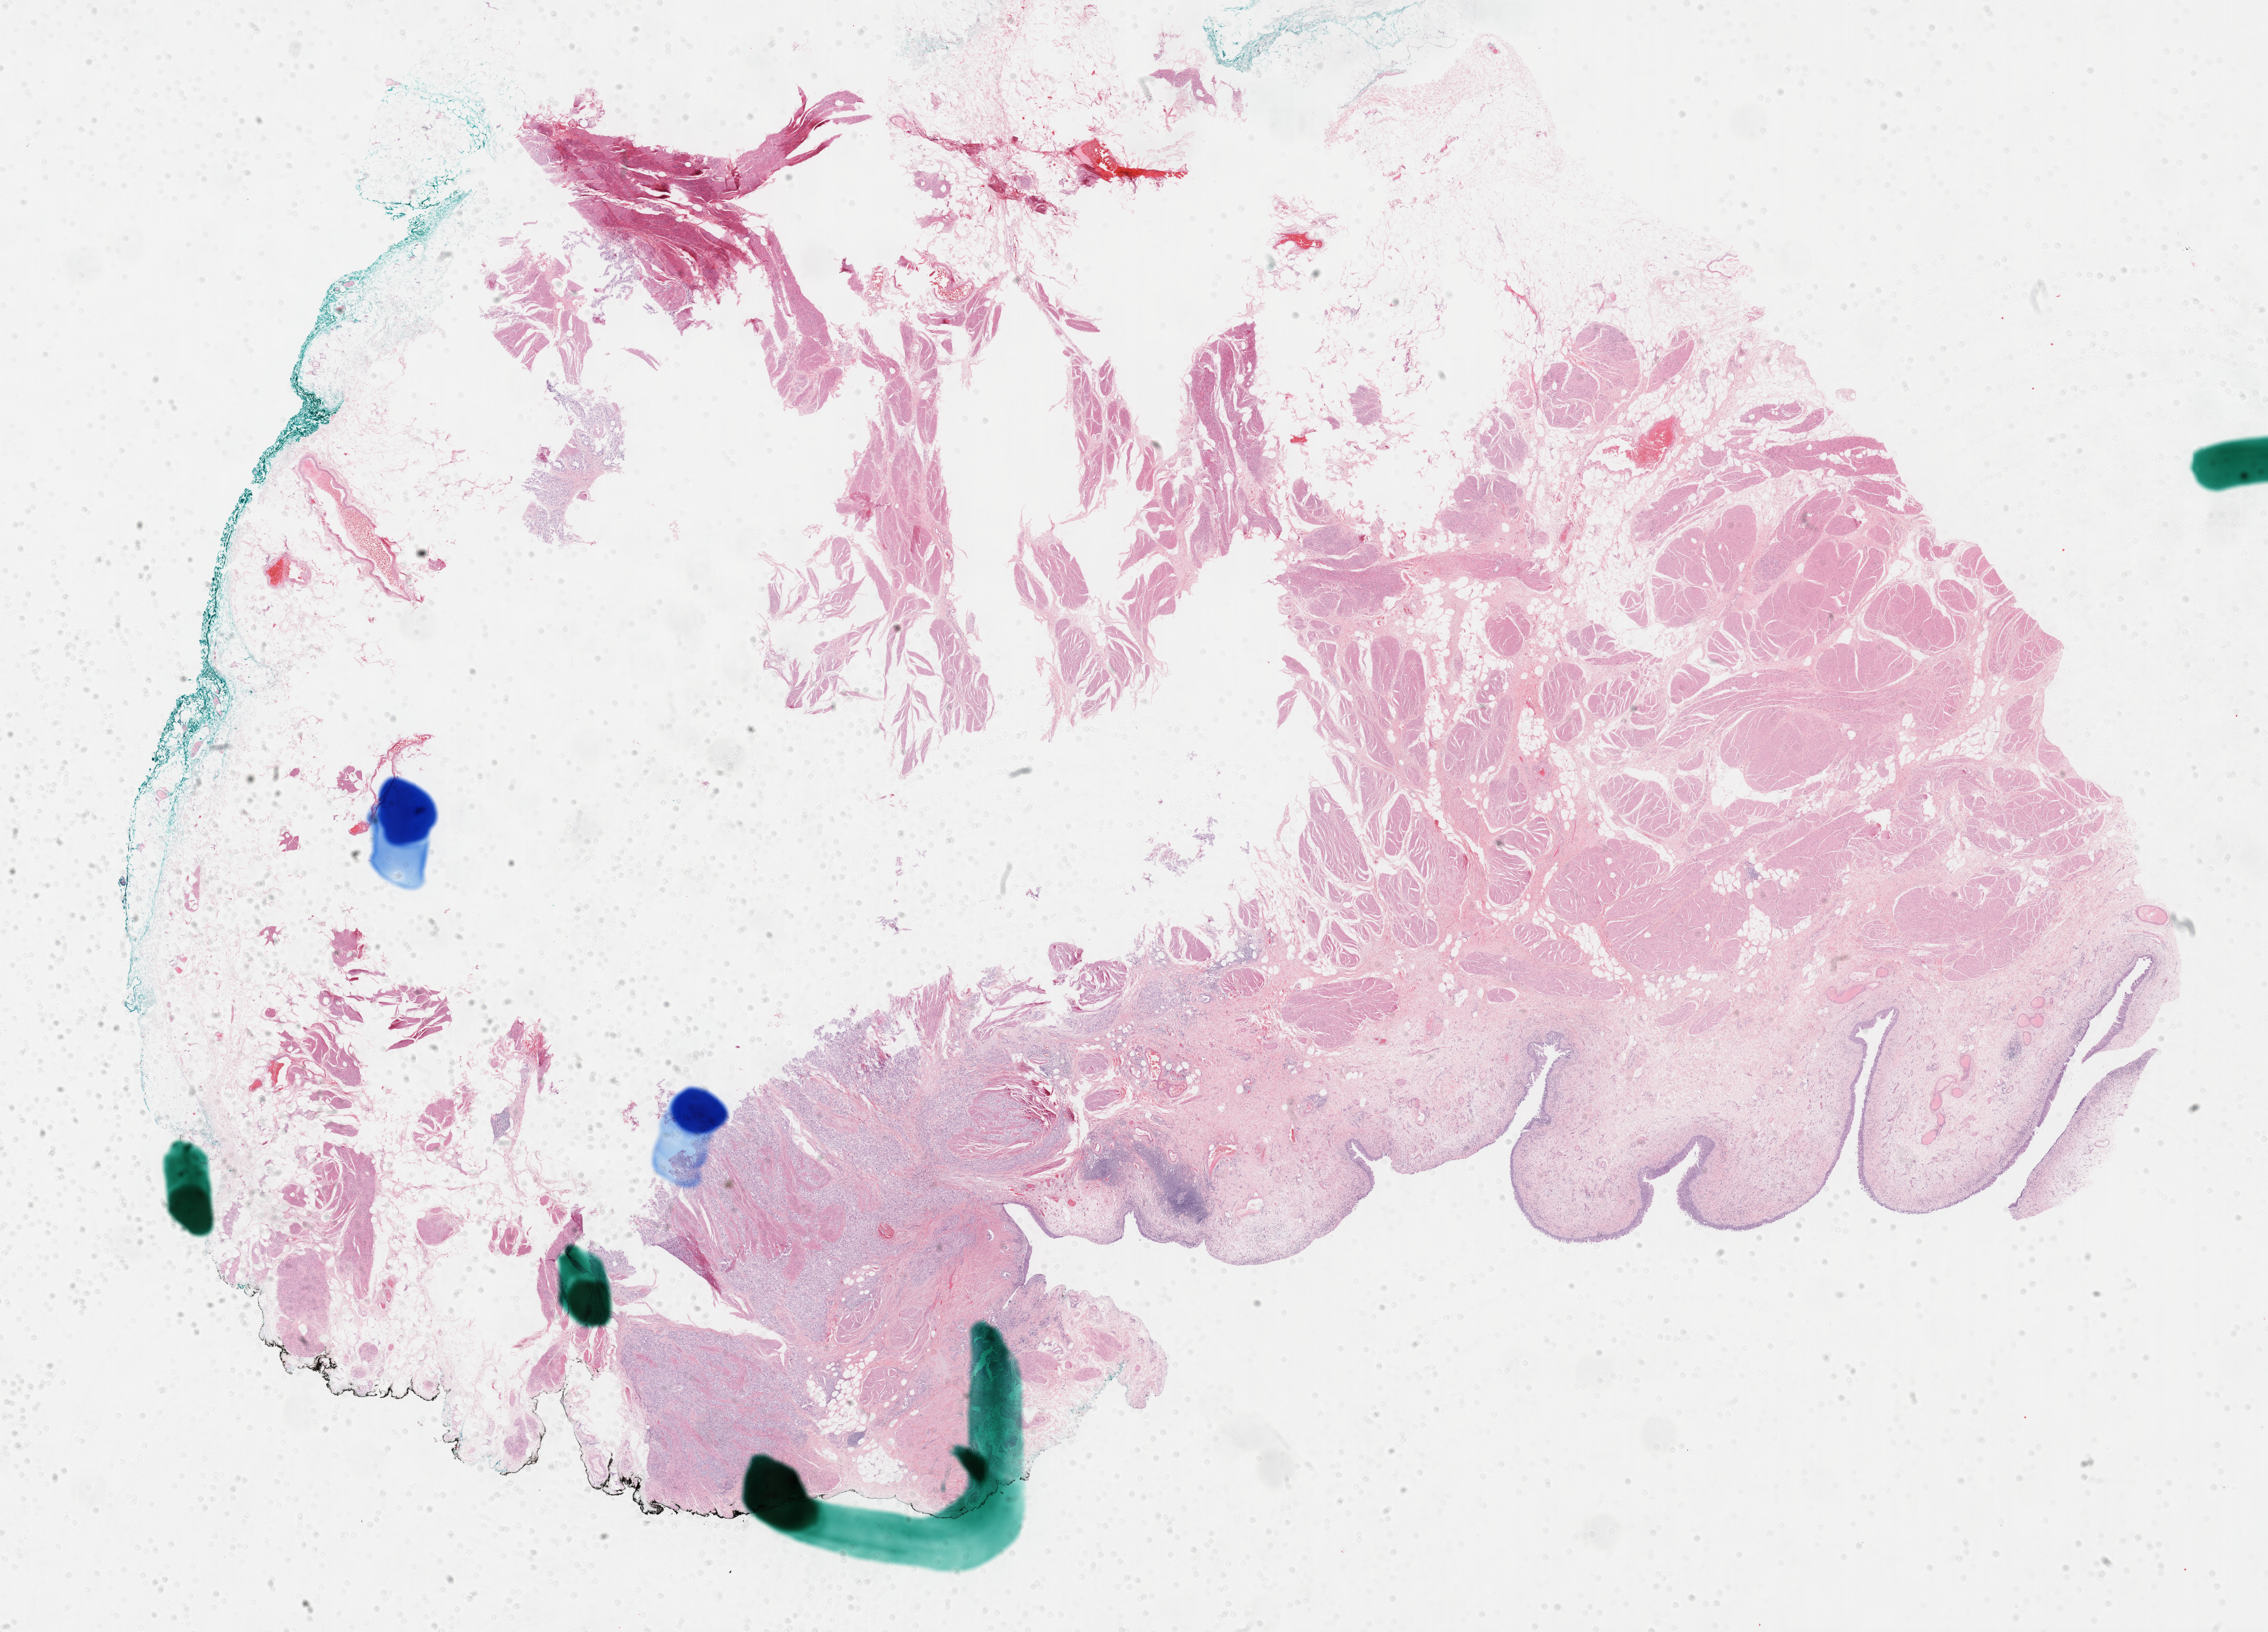
Whole-slide histology image, Hematoxylin and eosin (H&E) stained, whole scanned area (about 30.2 x 21.7 mm, slide scanned at 40x) shown as a low-resolution overview. FFPE section. Primary tumour sample from the bladder. Female patient; age at initial diagnosis 67 years. Histologic grade: high grade.
* pathologic diagnosis: Transitional cell carcinoma
* AJCC pathologic stage: II (6th edition)